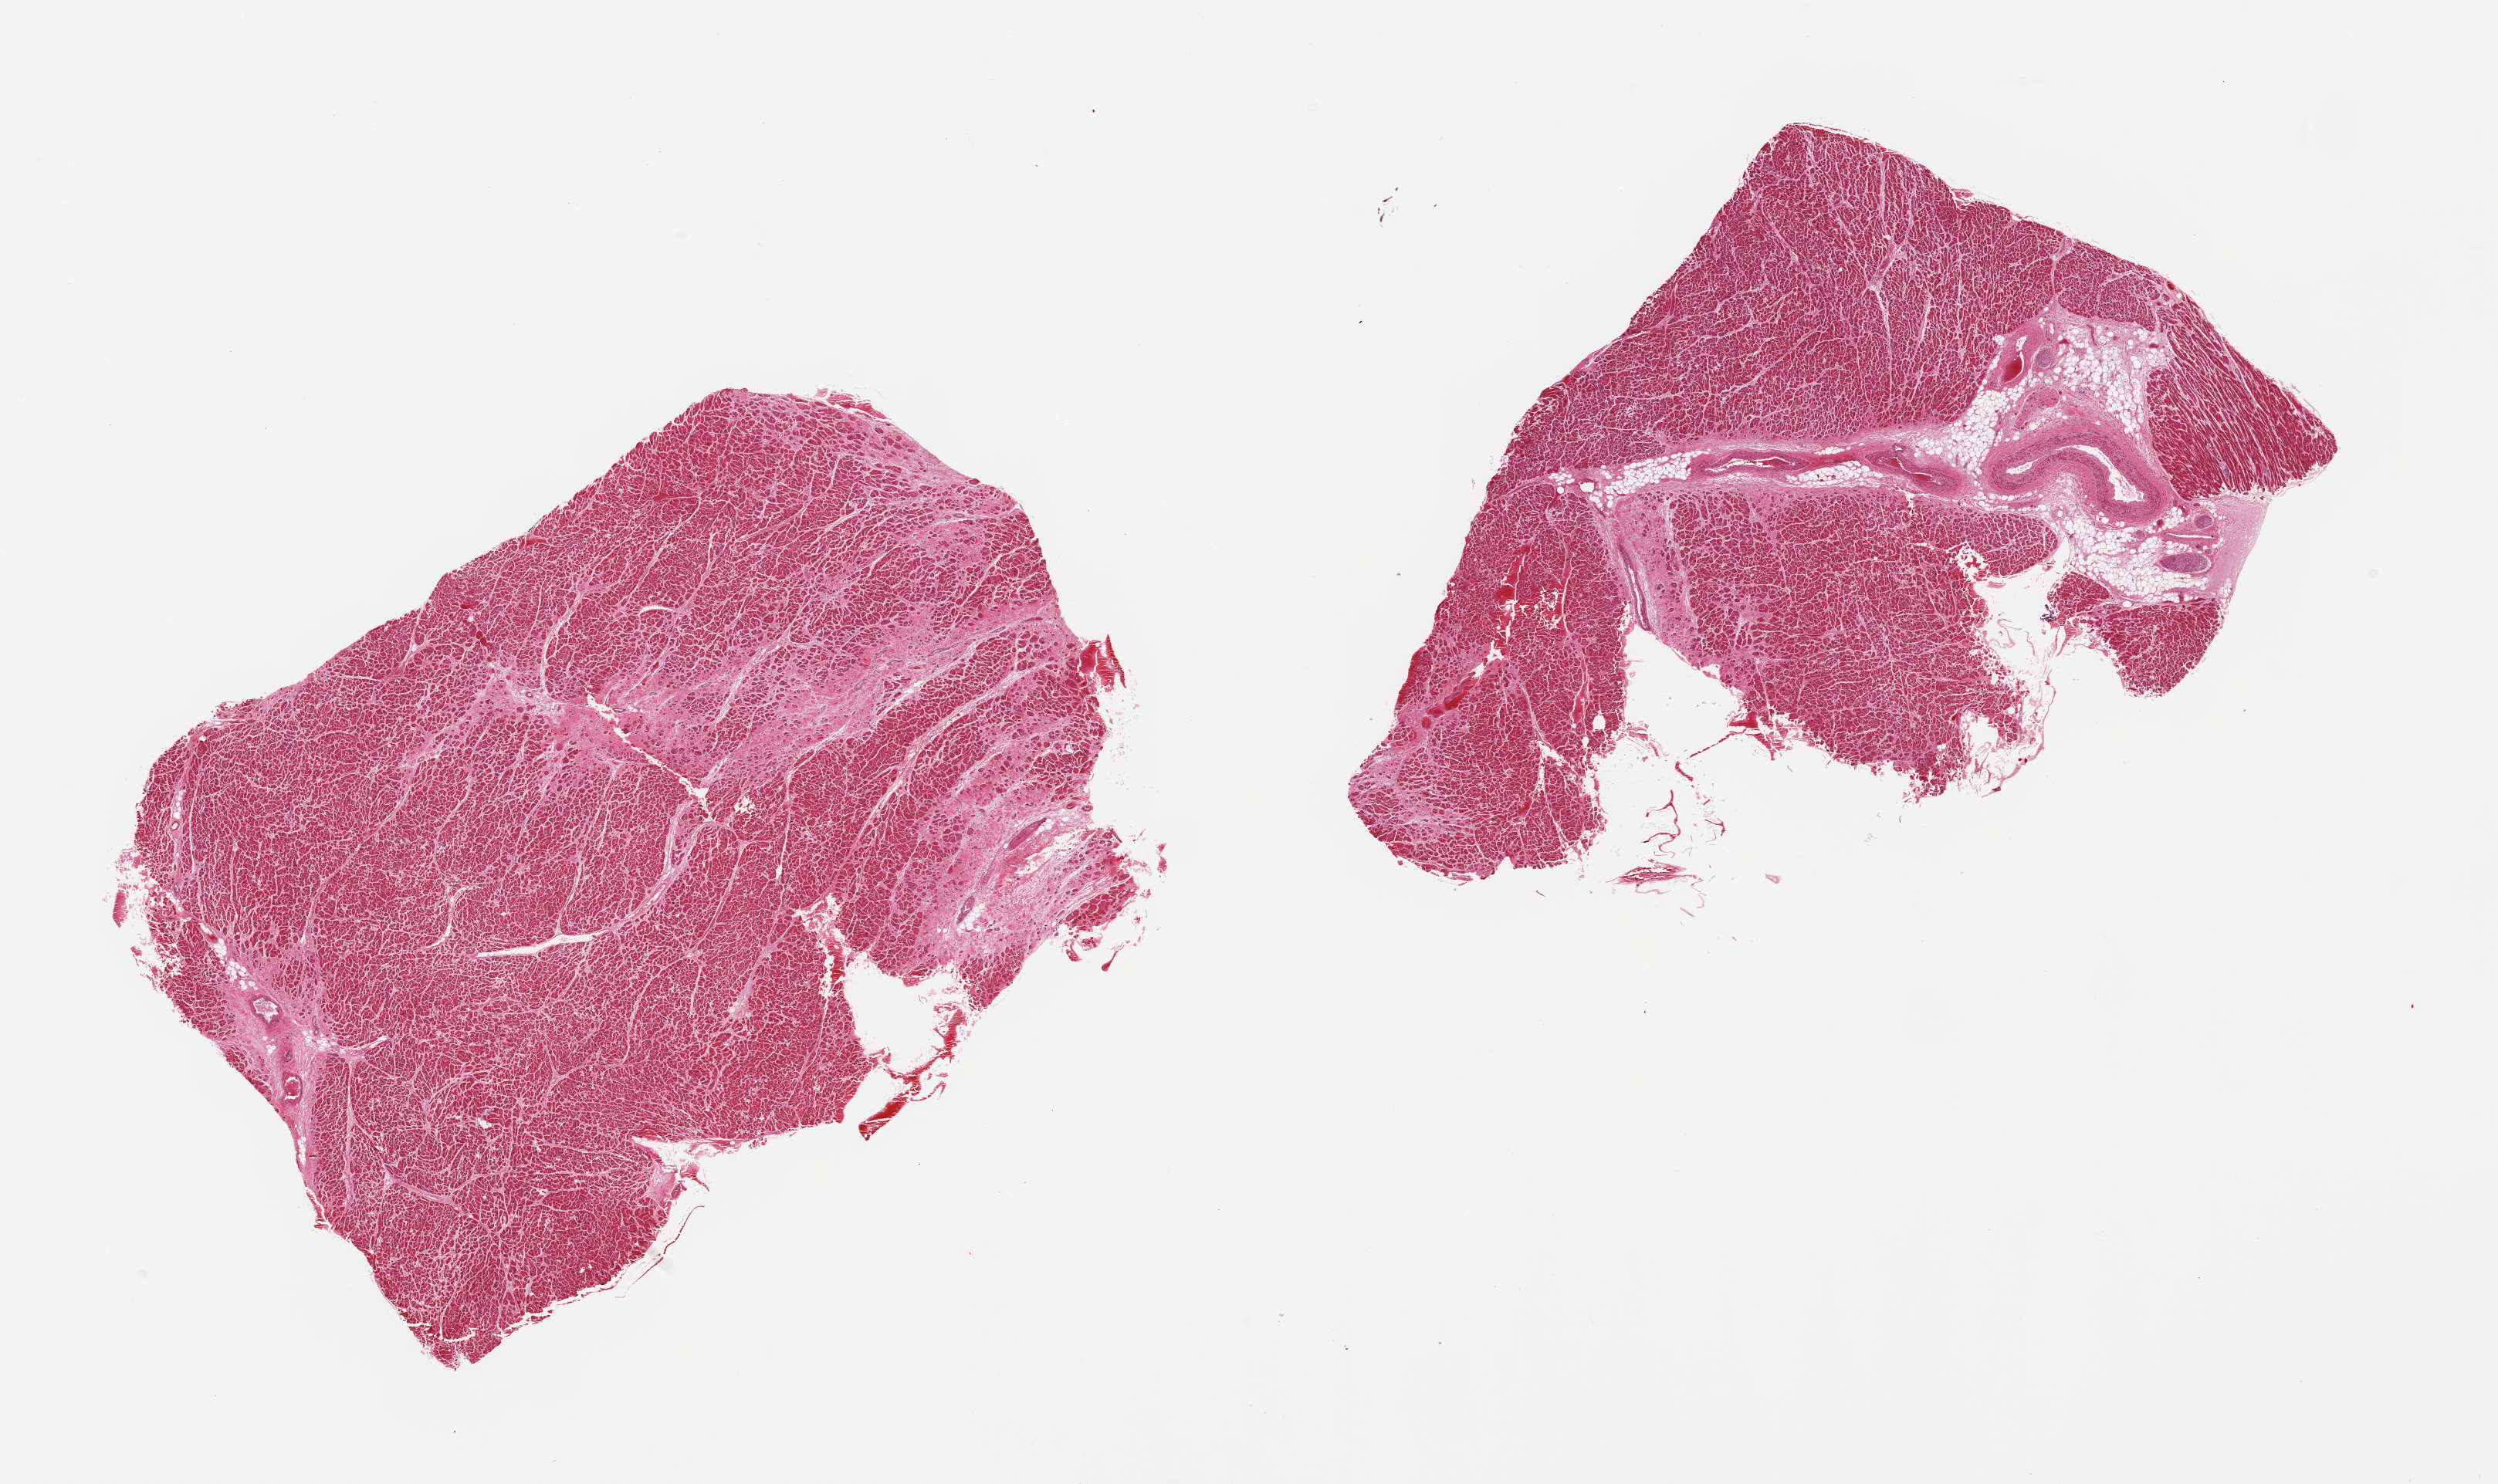
Hematoxylin and eosin (H&E) whole-slide image — whole scanned area (about 25.6 x 15.2 mm, from a 20x scan) shown as a low-resolution overview; PAXgene-fixed, paraffin-embedded tissue; target tissue: heart; donor tissue sample. Donor sex: male.
- pathologist's review note for this sample: 2 pieces; one with extensive fibrosis and scarring suggesting old infarct and other with large vessels, nerves and surrounding fat up to 30%, myocyte hypertrophy